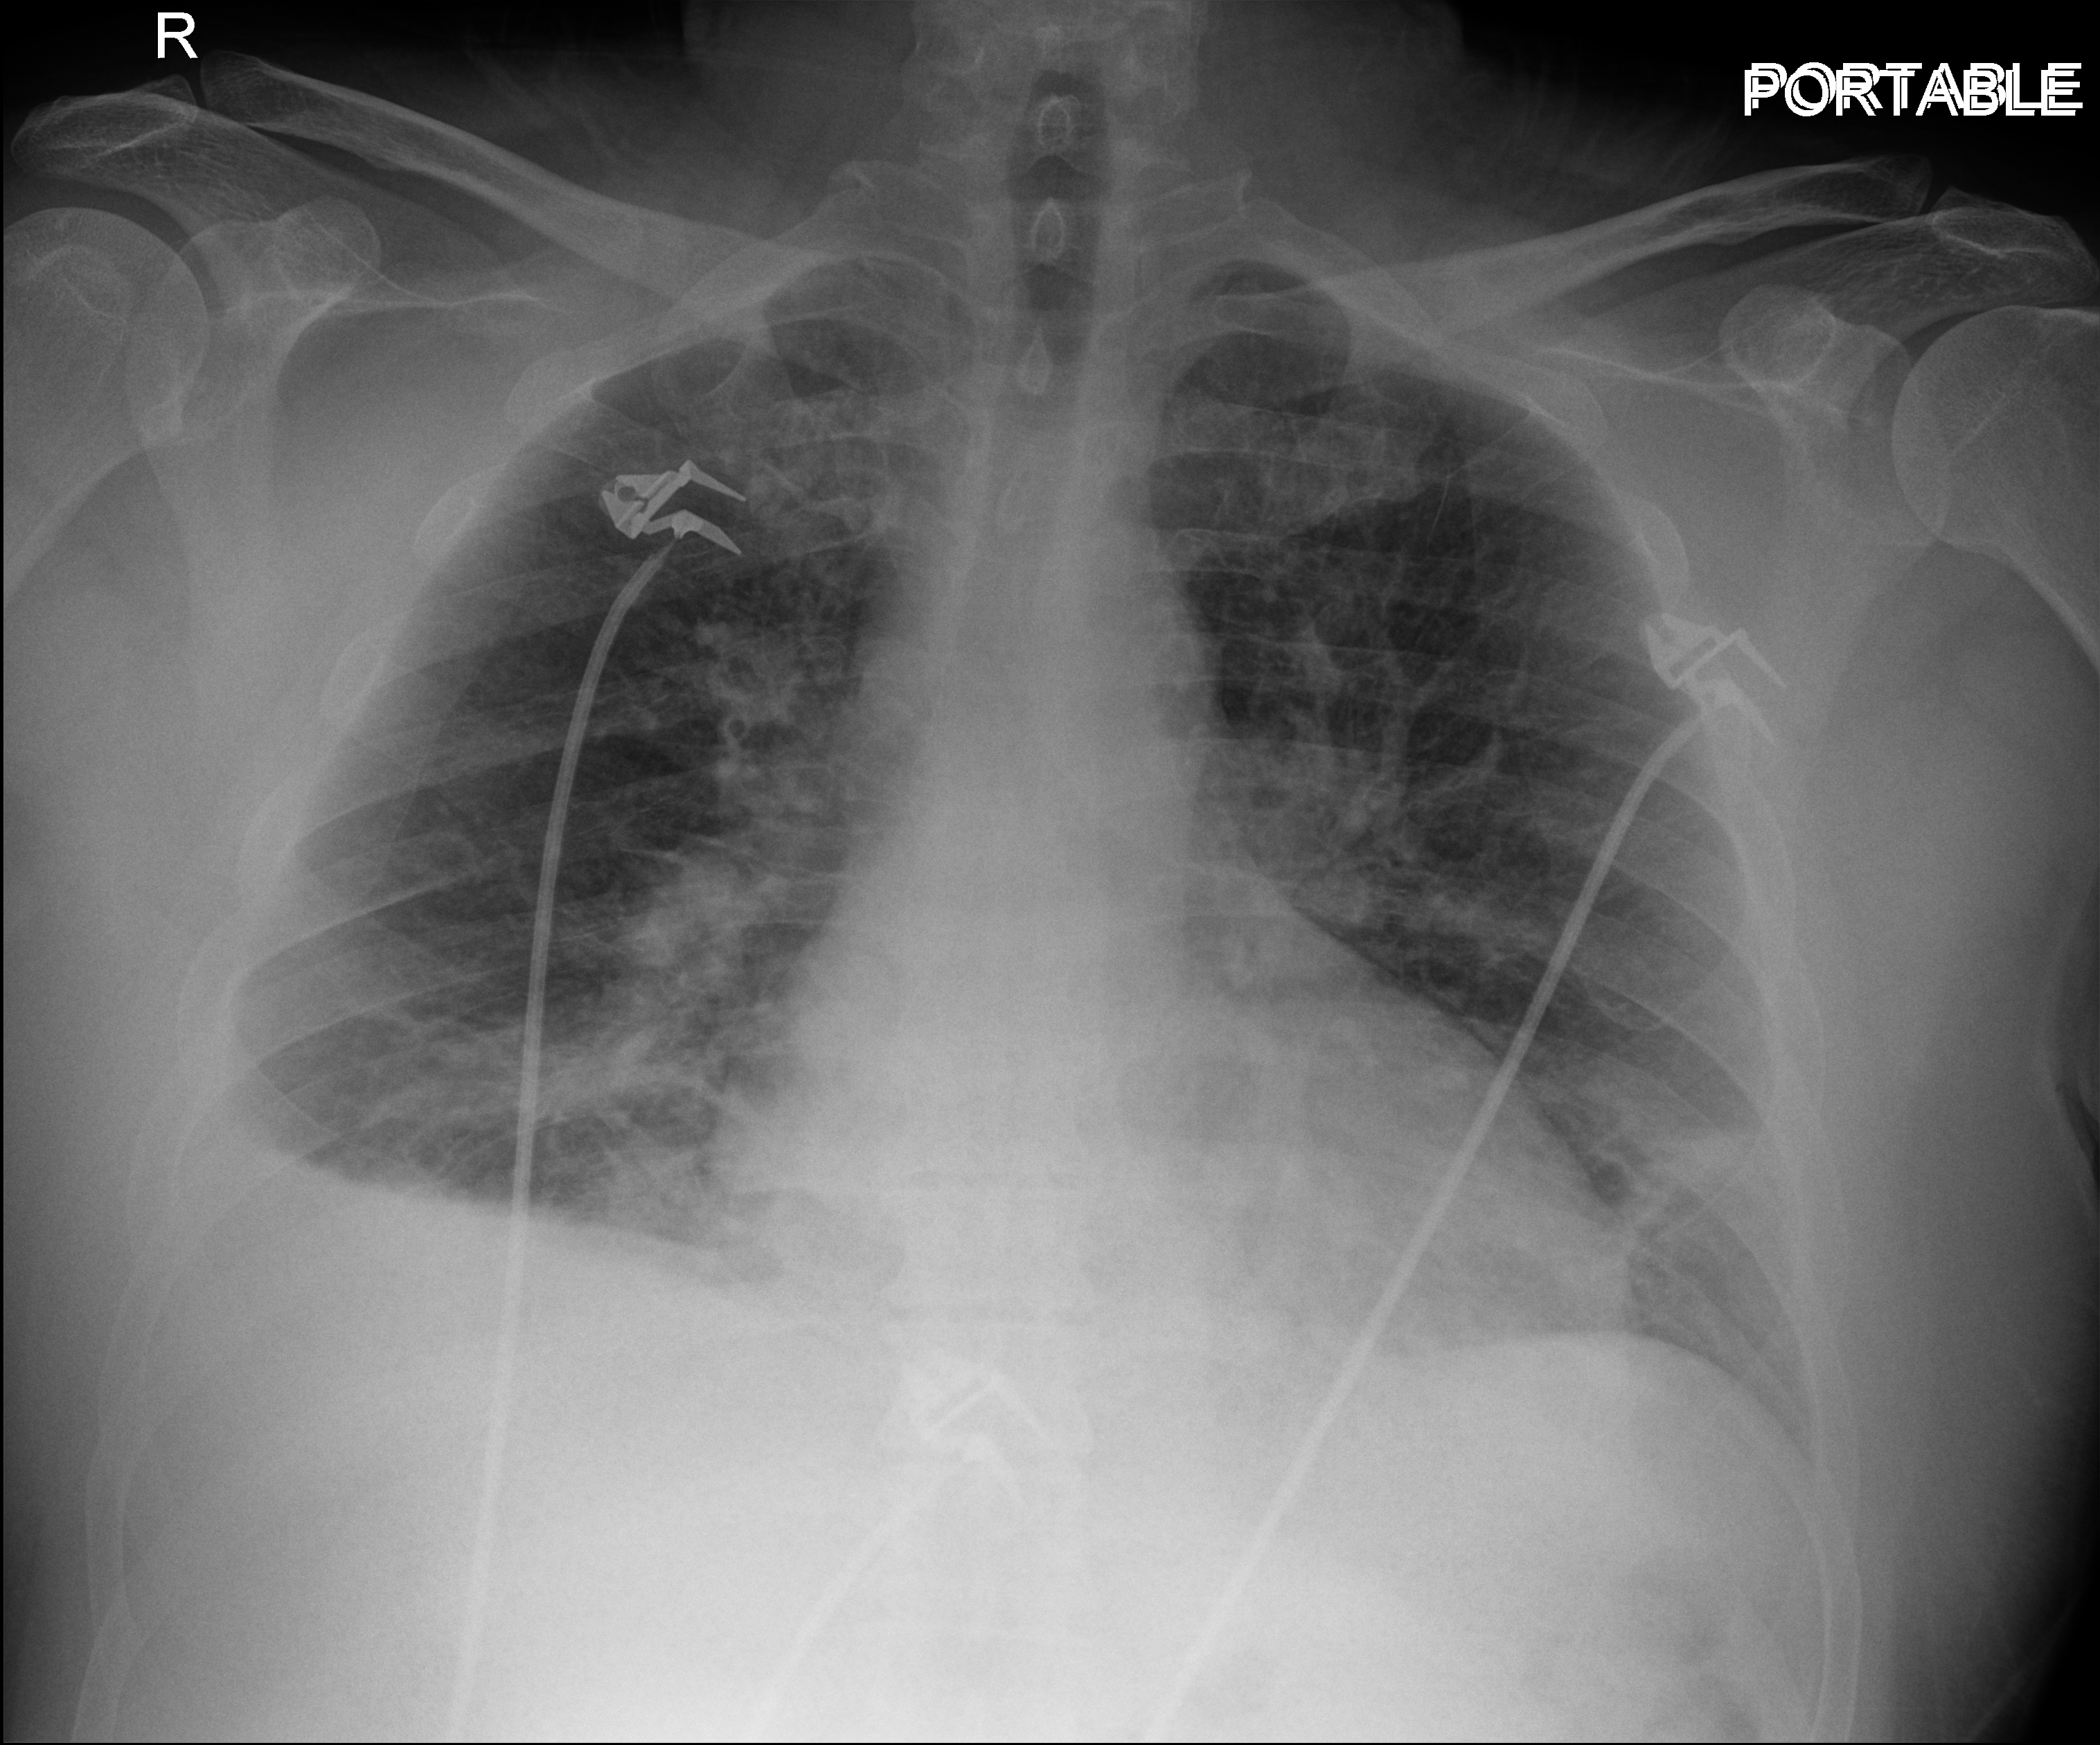
Chest X-ray (portable); anteroposterior (AP) projection. Patient hospitalised with COVID-19; male, aged 18–59 years.
Hospital-stay facts (about this admission, not read from this image; timing relative to this image not recorded): admitted to intensive care during this hospital stay: no.